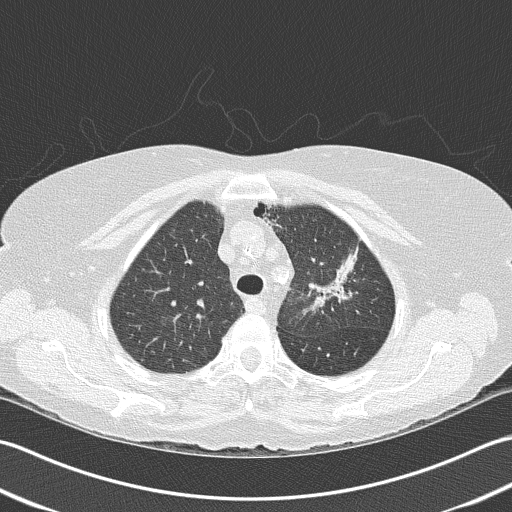
Axial slice from a low-dose chest CT screening exam; baseline screening round; lung window (W 1500 / L -600 HU); 2 mm slice thickness; 120 kVp; 512 × 512 image matrix. Female, age 68 years at enrolment.
- Expert-annotated lung lesion, bounding box (x1, y1, x2, y2) in pixels: (295, 236, 369, 316).
- Screening reader's record for this exam: no non-calcified nodule ≥4 mm recorded.